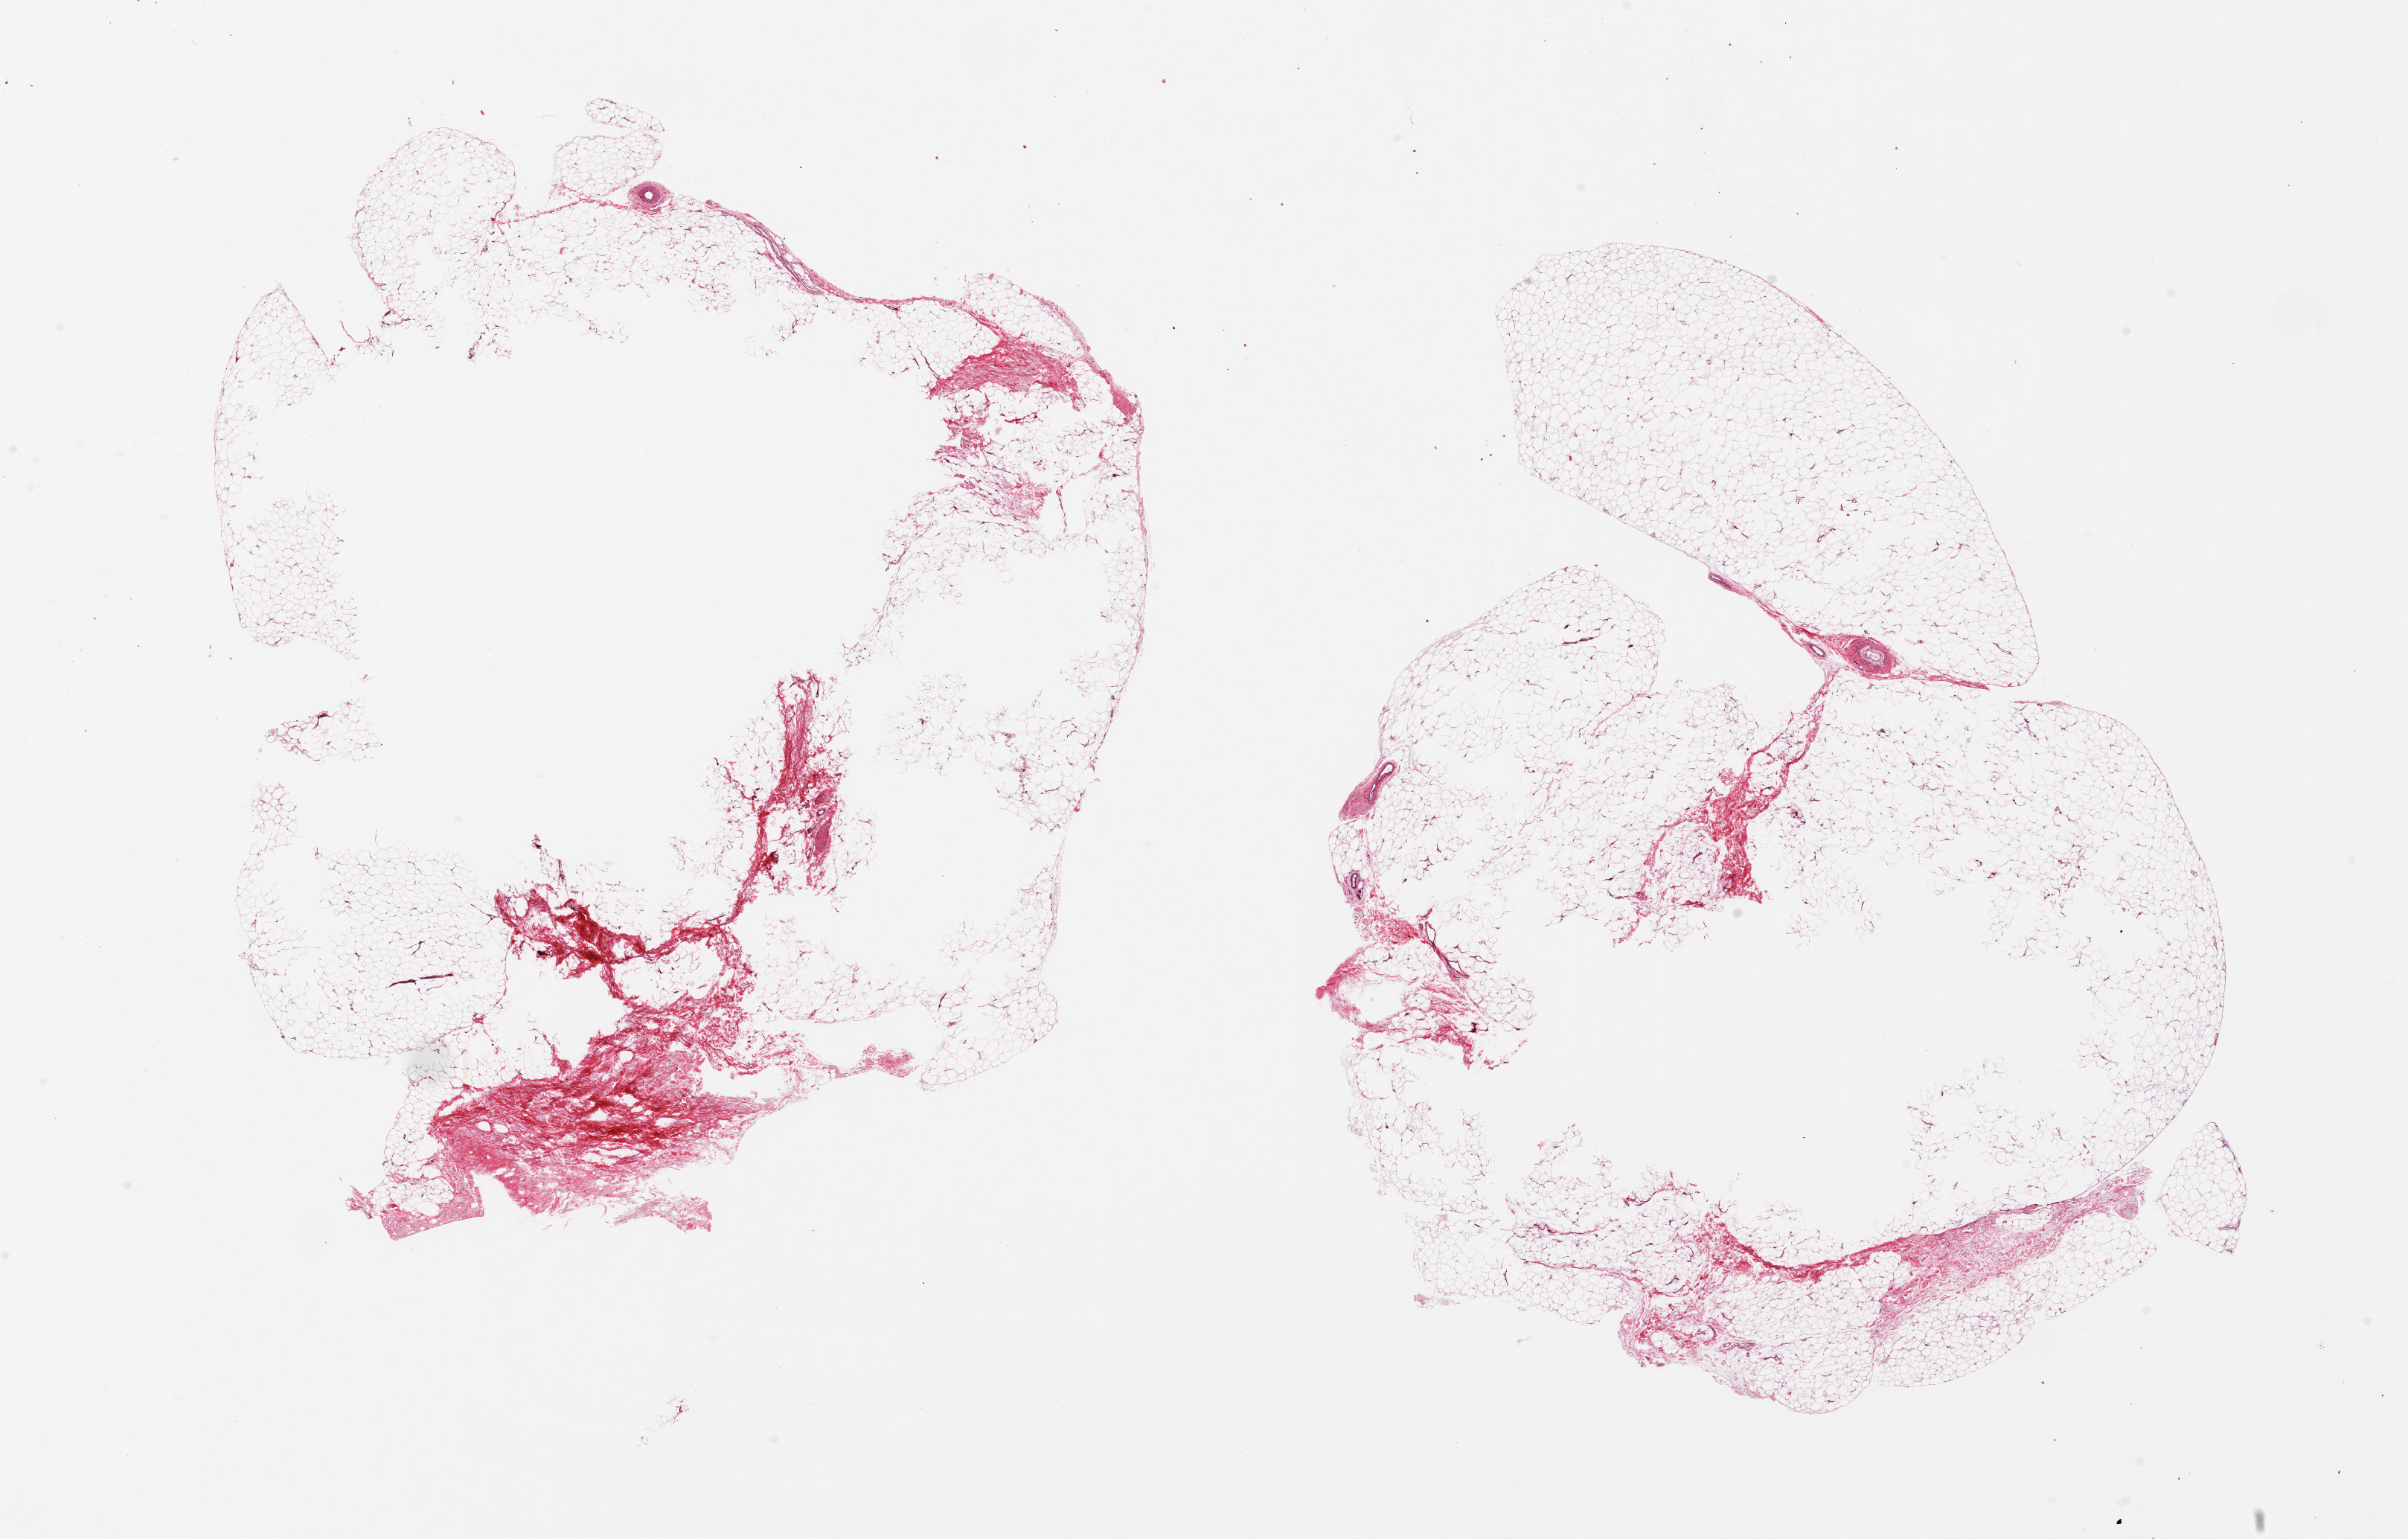
H&E whole-slide image — whole scanned area (about 25.6 x 16.4 mm) shown as a low-resolution overview. PAXgene-fixed, paraffin-embedded tissue. Target tissue: adipose tissue. Tissue donor sample. Donor: male.
- pathologist's review note for this sample: 2 pieces 12x9 & 11x10 mm; large central unfixed empty zones 40-50% of aliquots